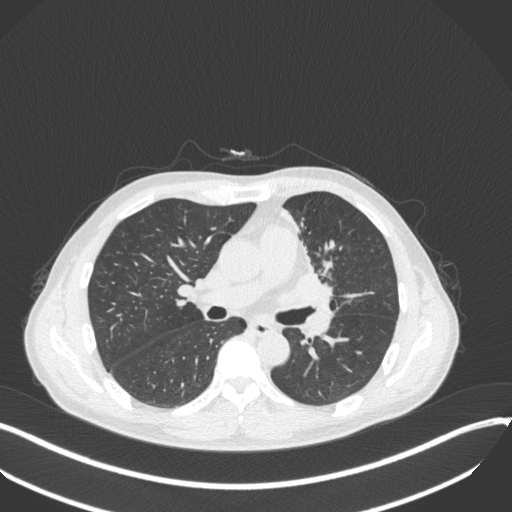
Chest CT, one axial slice; slice 189 of 411 in the series (ordered by position); reconstruction kernel B31f; 120 kVp; lung window (W 1500 / L -600 HU); 1 mm slice thickness; 512 × 512 image matrix. Patient: male, 56 years. Case-level facts recorded for this patient, not image findings: clinical TNM (as recorded): T2a N0 M0.
Annotated regions visible in this slice (bounding box drawn by a radiologist):
- lung tumour (recorded histology: squamous cell carcinoma): bounding box [x1, y1, x2, y2] px = [280, 266, 344, 311]